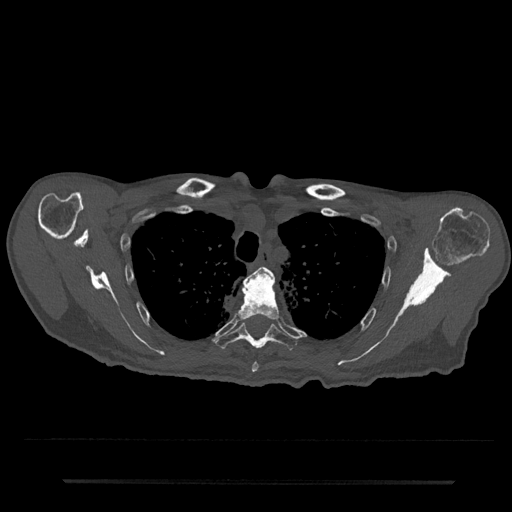
CT including the spine, one axial slice; position 603 of 797 along the scan axis; reconstruction kernel Br40s/3; 120 kVp; bone window (W 1800 / L 400 HU); 0.5 mm slice thickness; 512 × 512 image matrix, field of view 427 × 427 mm. Male patient, age 74 years. Case-level facts recorded for this patient, not image findings: primary cancer: prostate.
Structures marked on this image (semi-automatic segmentation, software-assisted and operator-edited):
- T3 vertebra: bounding box [x1, y1, x2, y2] px = [262, 267, 274, 279]
- T4 vertebra: [237, 269, 279, 373]
- T5 vertebra: [215, 319, 298, 351]